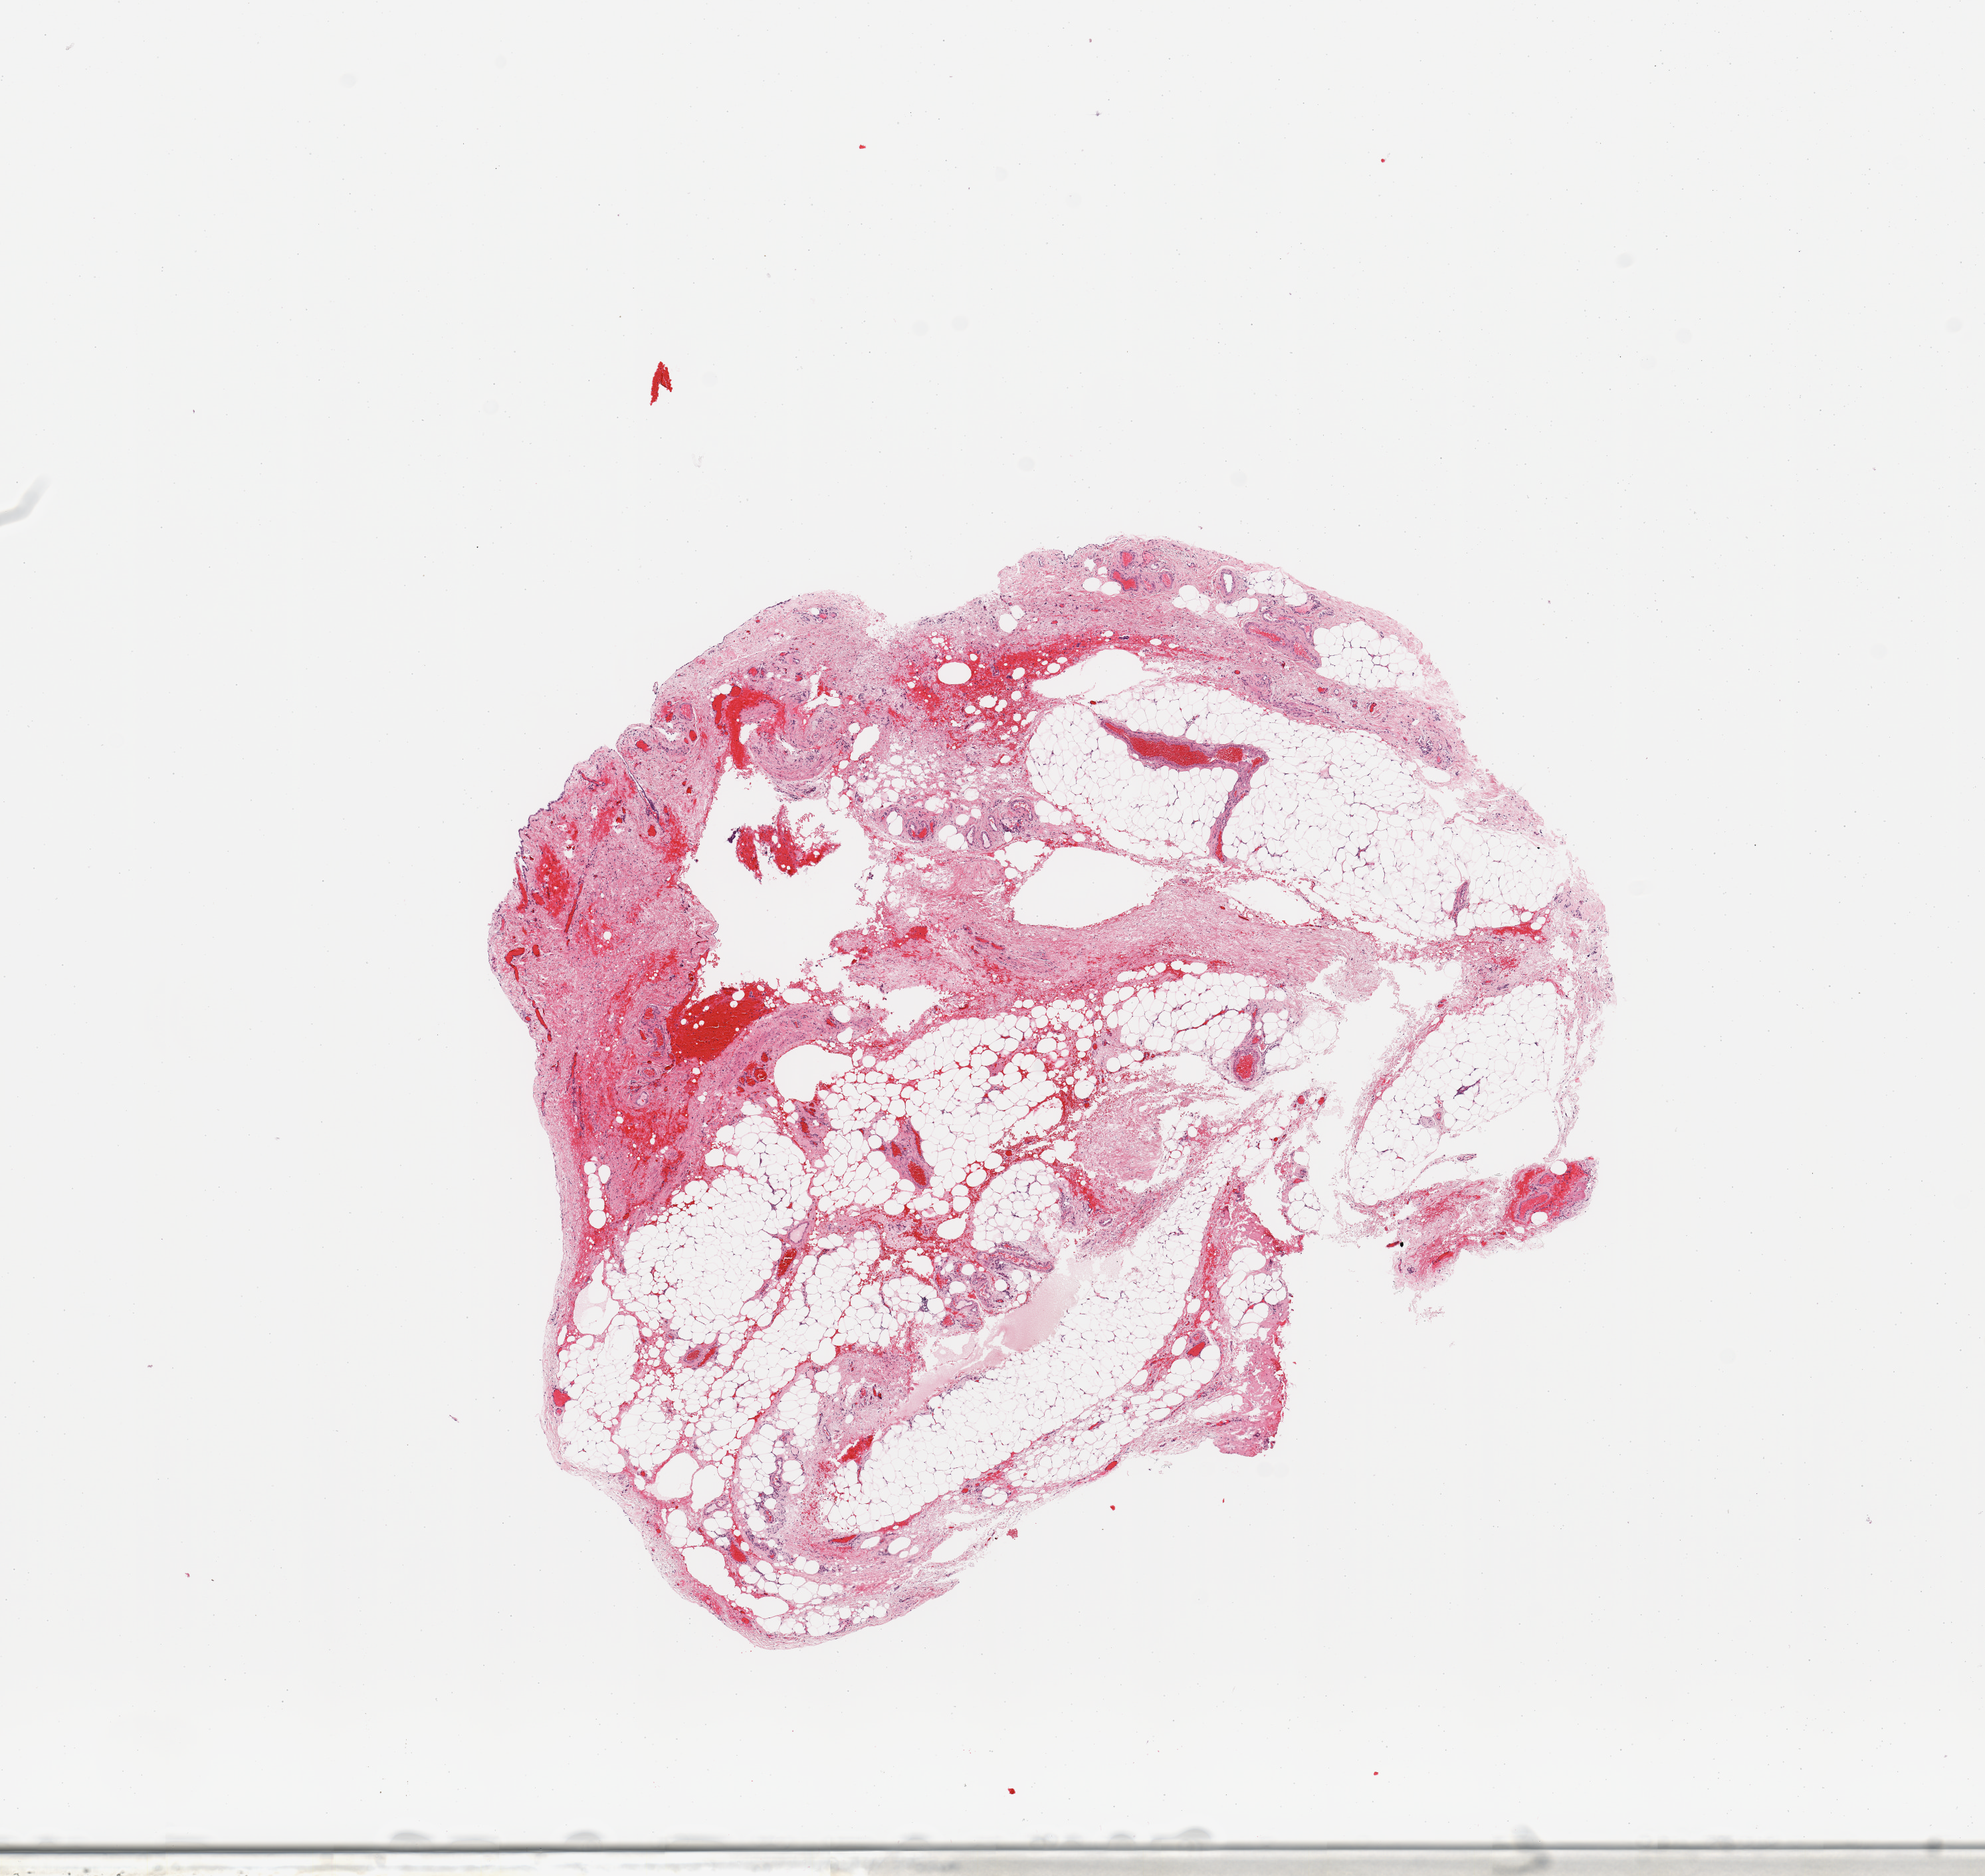
H&E-stained whole-slide image, shown as a low-resolution overview of the whole scanned area (about 11.8 x 11.2 mm, acquisition: 20x scan), uterus, normal (non-tumour) tissue. Female, 60 y/o.
• this section: normal (non-tumour) tissue from the same patient
• patient diagnosis: Endometrioid adenocarcinoma, NOS